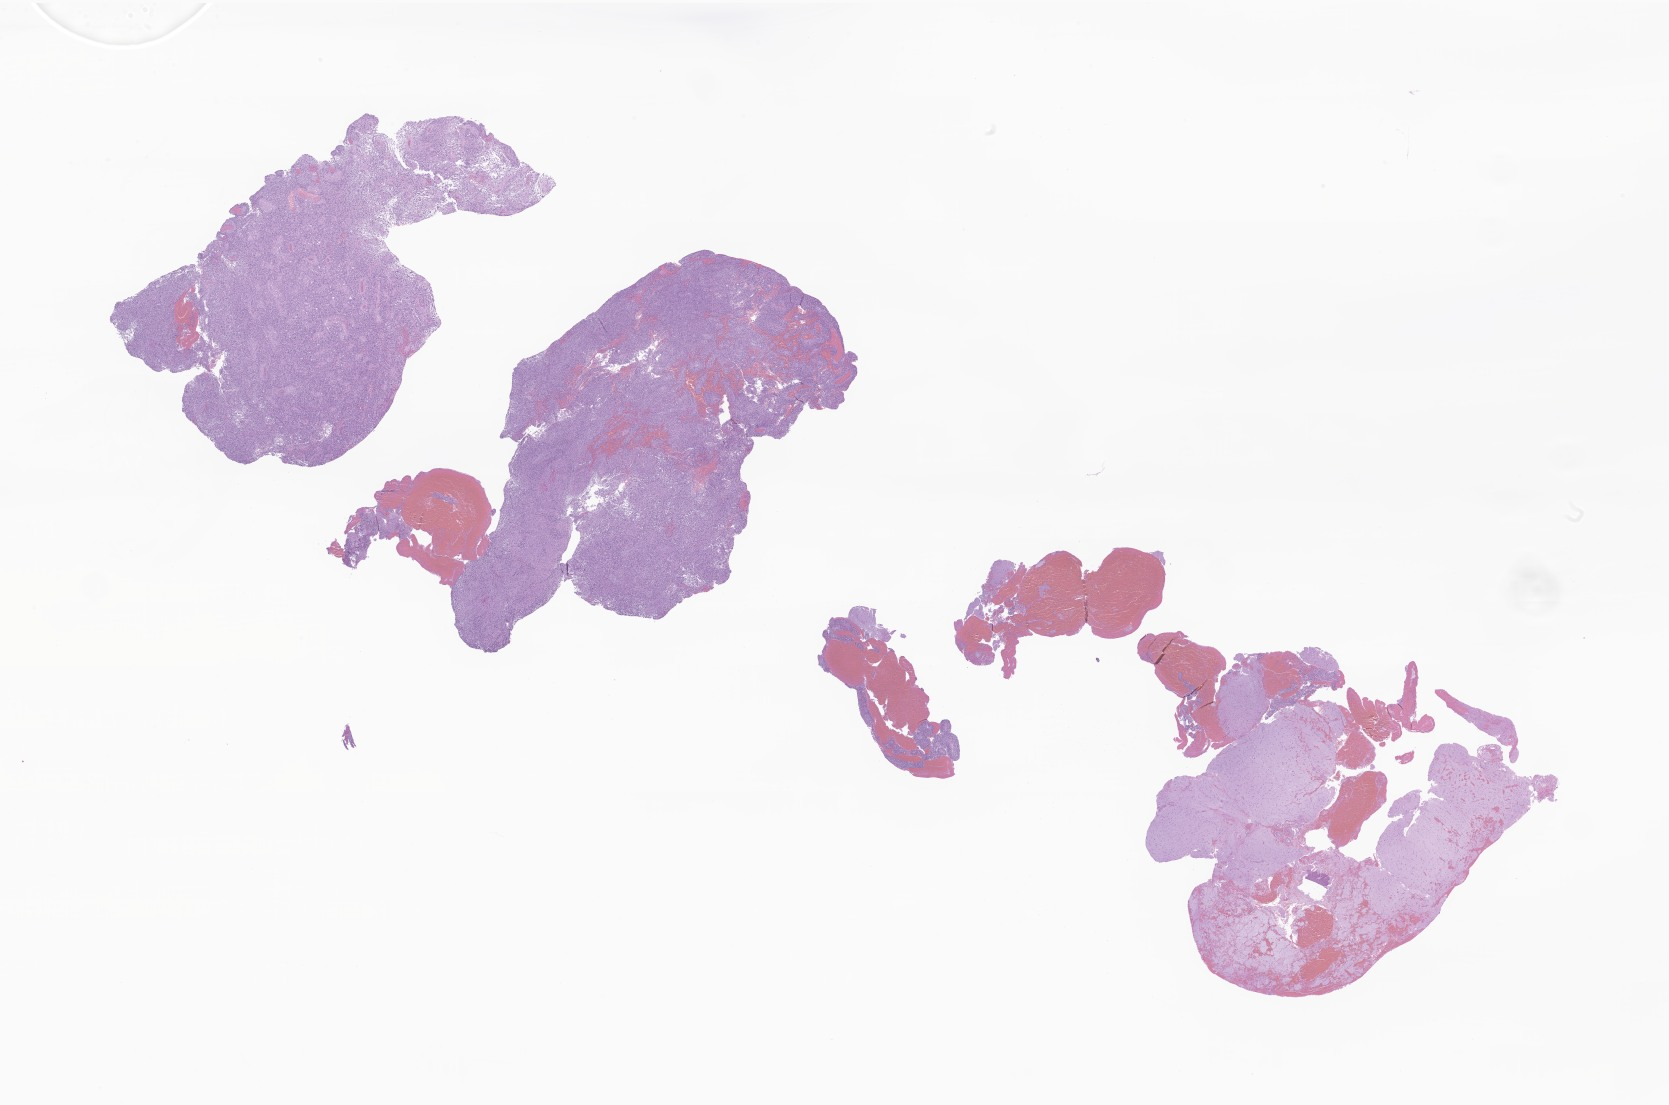
Digitized hematoxylin and eosin (H&E)-stained section of tumor tissue from the brain — a low-resolution overview of the entire scanned area, about 28.1 x 18.6 mm. FFPE section. Male patient, age 129 months (10 years 9 months).
Diagnosis: Glioma, malignant.